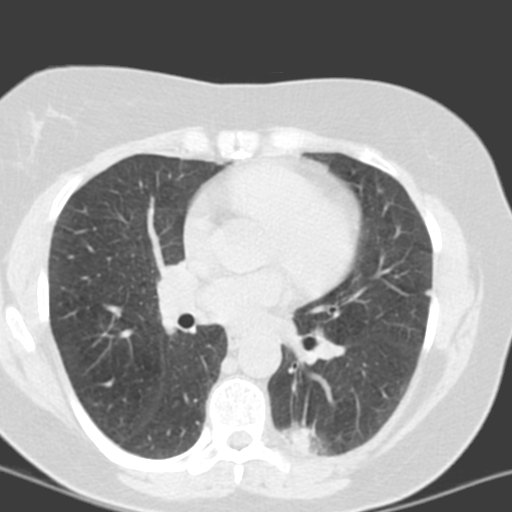
Low-dose screening chest CT, one axial slice. Slice 84 of 150 in the series (ordered by position). 120 kVp. Lung window (W 1500 / L -600 HU). 3.2 mm slice thickness. 512 × 512 image matrix.
Annotated regions visible in this slice (outlined manually by an expert reader):
- lesion 2 (tumor, lower lobe of left lung): bounding box (x1, y1, x2, y2) in pixels: (287, 428, 313, 450)